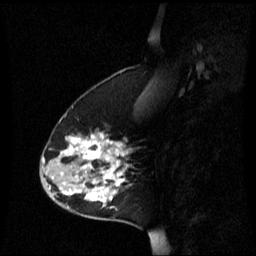
Breast MRI (dynamic contrast-enhanced), one sagittal slice. Position 21 of 60 along the scan axis. Dynamic contrast-enhanced series, image 2 of 3 at this slice position (ordered by acquisition). 1.5 T. TE 4.2 ms, TR 8.4 ms. 256 × 256 image matrix, field of view 240 × 240 mm. Patient: female, 45 years. From the clinical record (not read from this slice): setting: breast cancer imaged before/during neoadjuvant chemotherapy; receptor status: HR-positive, HER2-negative.
Outlined on this slice (semi-automatically segmented with operator editing):
- analysis volume of interest (the breast-tissue region the enhancement analysis was run in; not a lesion): box from (x=40, y=132) to (x=131, y=221) px
- tumour enhancement mask (voxels above the 70 % enhancement threshold inside the analysis volume of interest): (x=50, y=134)–(x=129, y=207)